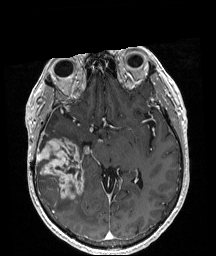
Brain MRI from a brain-tumour surgery series, one axial slice. Position 113 of 208 along the scan axis. T1-weighted post-contrast. 1 mm slice thickness. 216 × 256 image matrix, field of view 211 × 250 mm. Case-level facts recorded for this patient, not image findings: histopathology: Astrocytoma; WHO grade: 4; IDH mutation: yes; tumour location: Right Temporal.
Structures marked on this image (manually delineated by an expert):
- tumour: bounding box <36,138,83,200> (left, top, right, bottom; pixels)